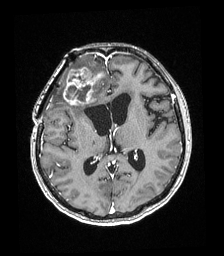
Brain MRI from a brain-tumour surgery series, one axial slice. Slice 93 of 192 in the series (ordered by position). T1-weighted post-contrast. 224 × 256 image matrix, field of view 219 × 250 mm. Case-level facts recorded for this patient, not image findings: histopathology: Astrocytoma; WHO grade: 4; IDH mutation: yes; tumour location: Right superficial frontal.
Structures marked on this image (outlined manually by an expert reader):
- tumour: box from (x=63, y=60) to (x=101, y=105) px